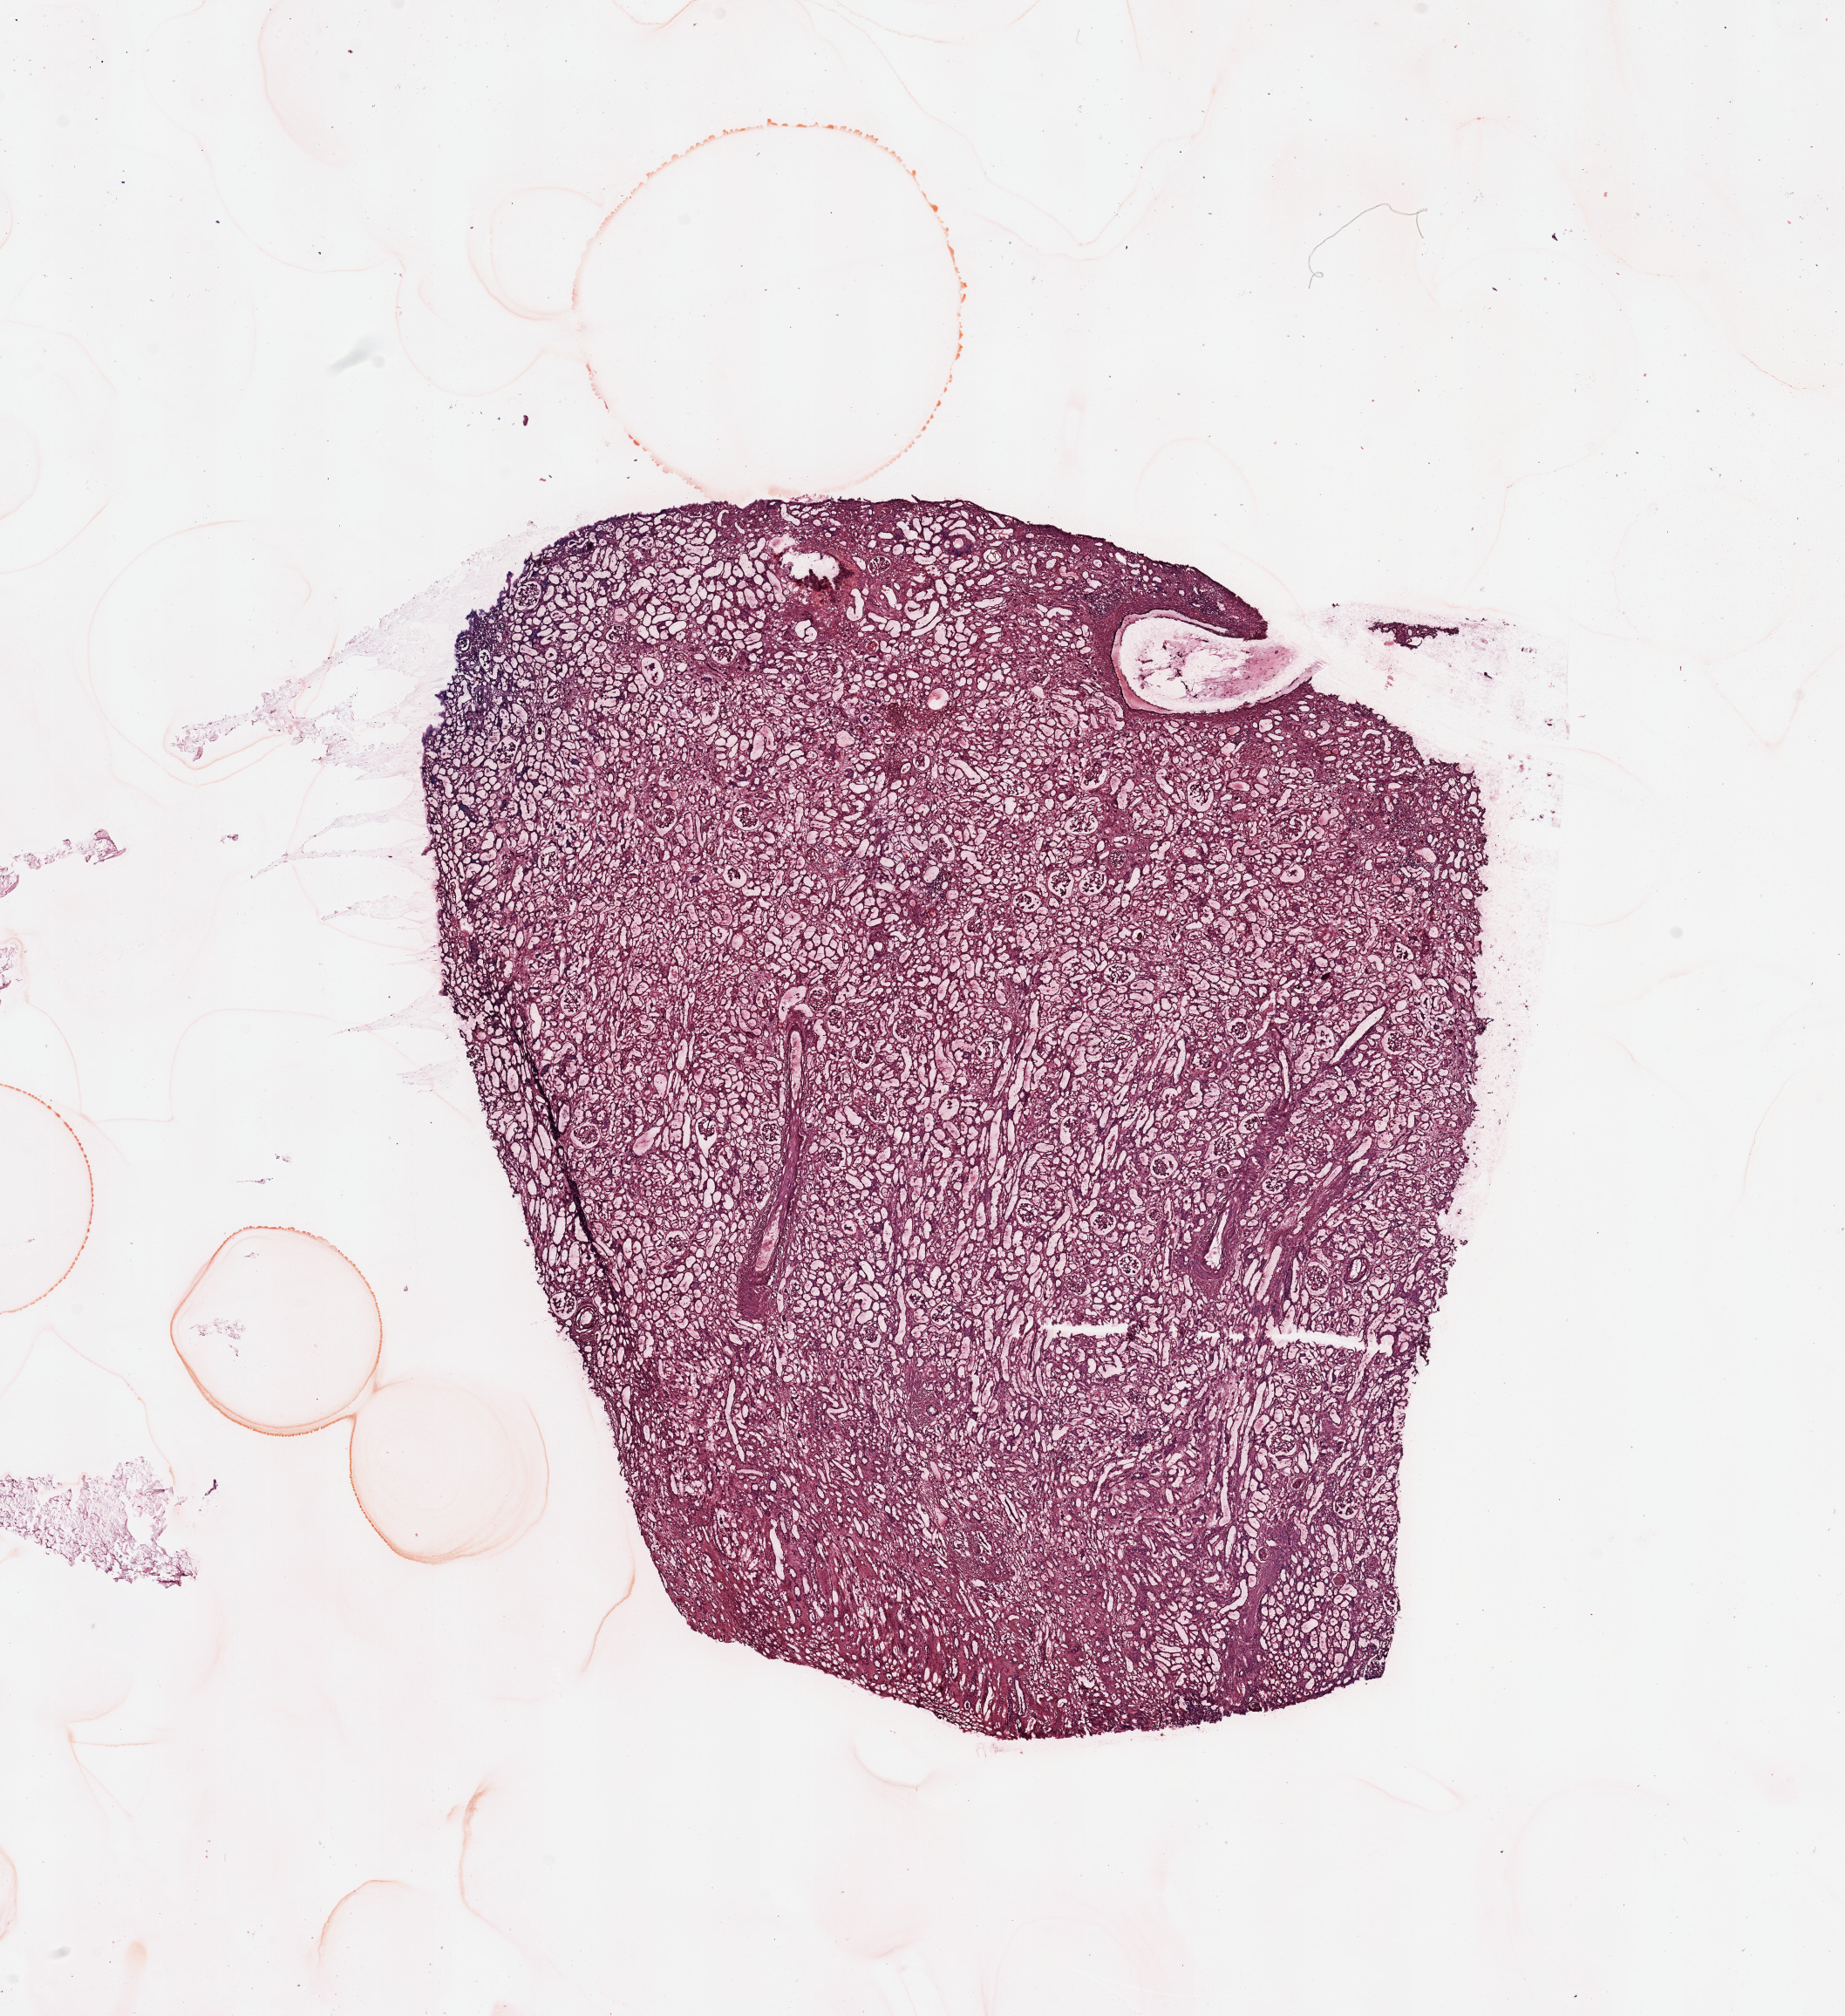
H&E whole-slide image — a low-resolution overview of the entire scanned area, about 16.7 x 18.3 mm (from a 20x scan), normal (non-tumour) tissue sample, sampled site: kidney. Patient: male, age 72 years.
This section: normal (non-tumour) tissue from the same patient. Patient diagnosis: Renal cell carcinoma, NOS.